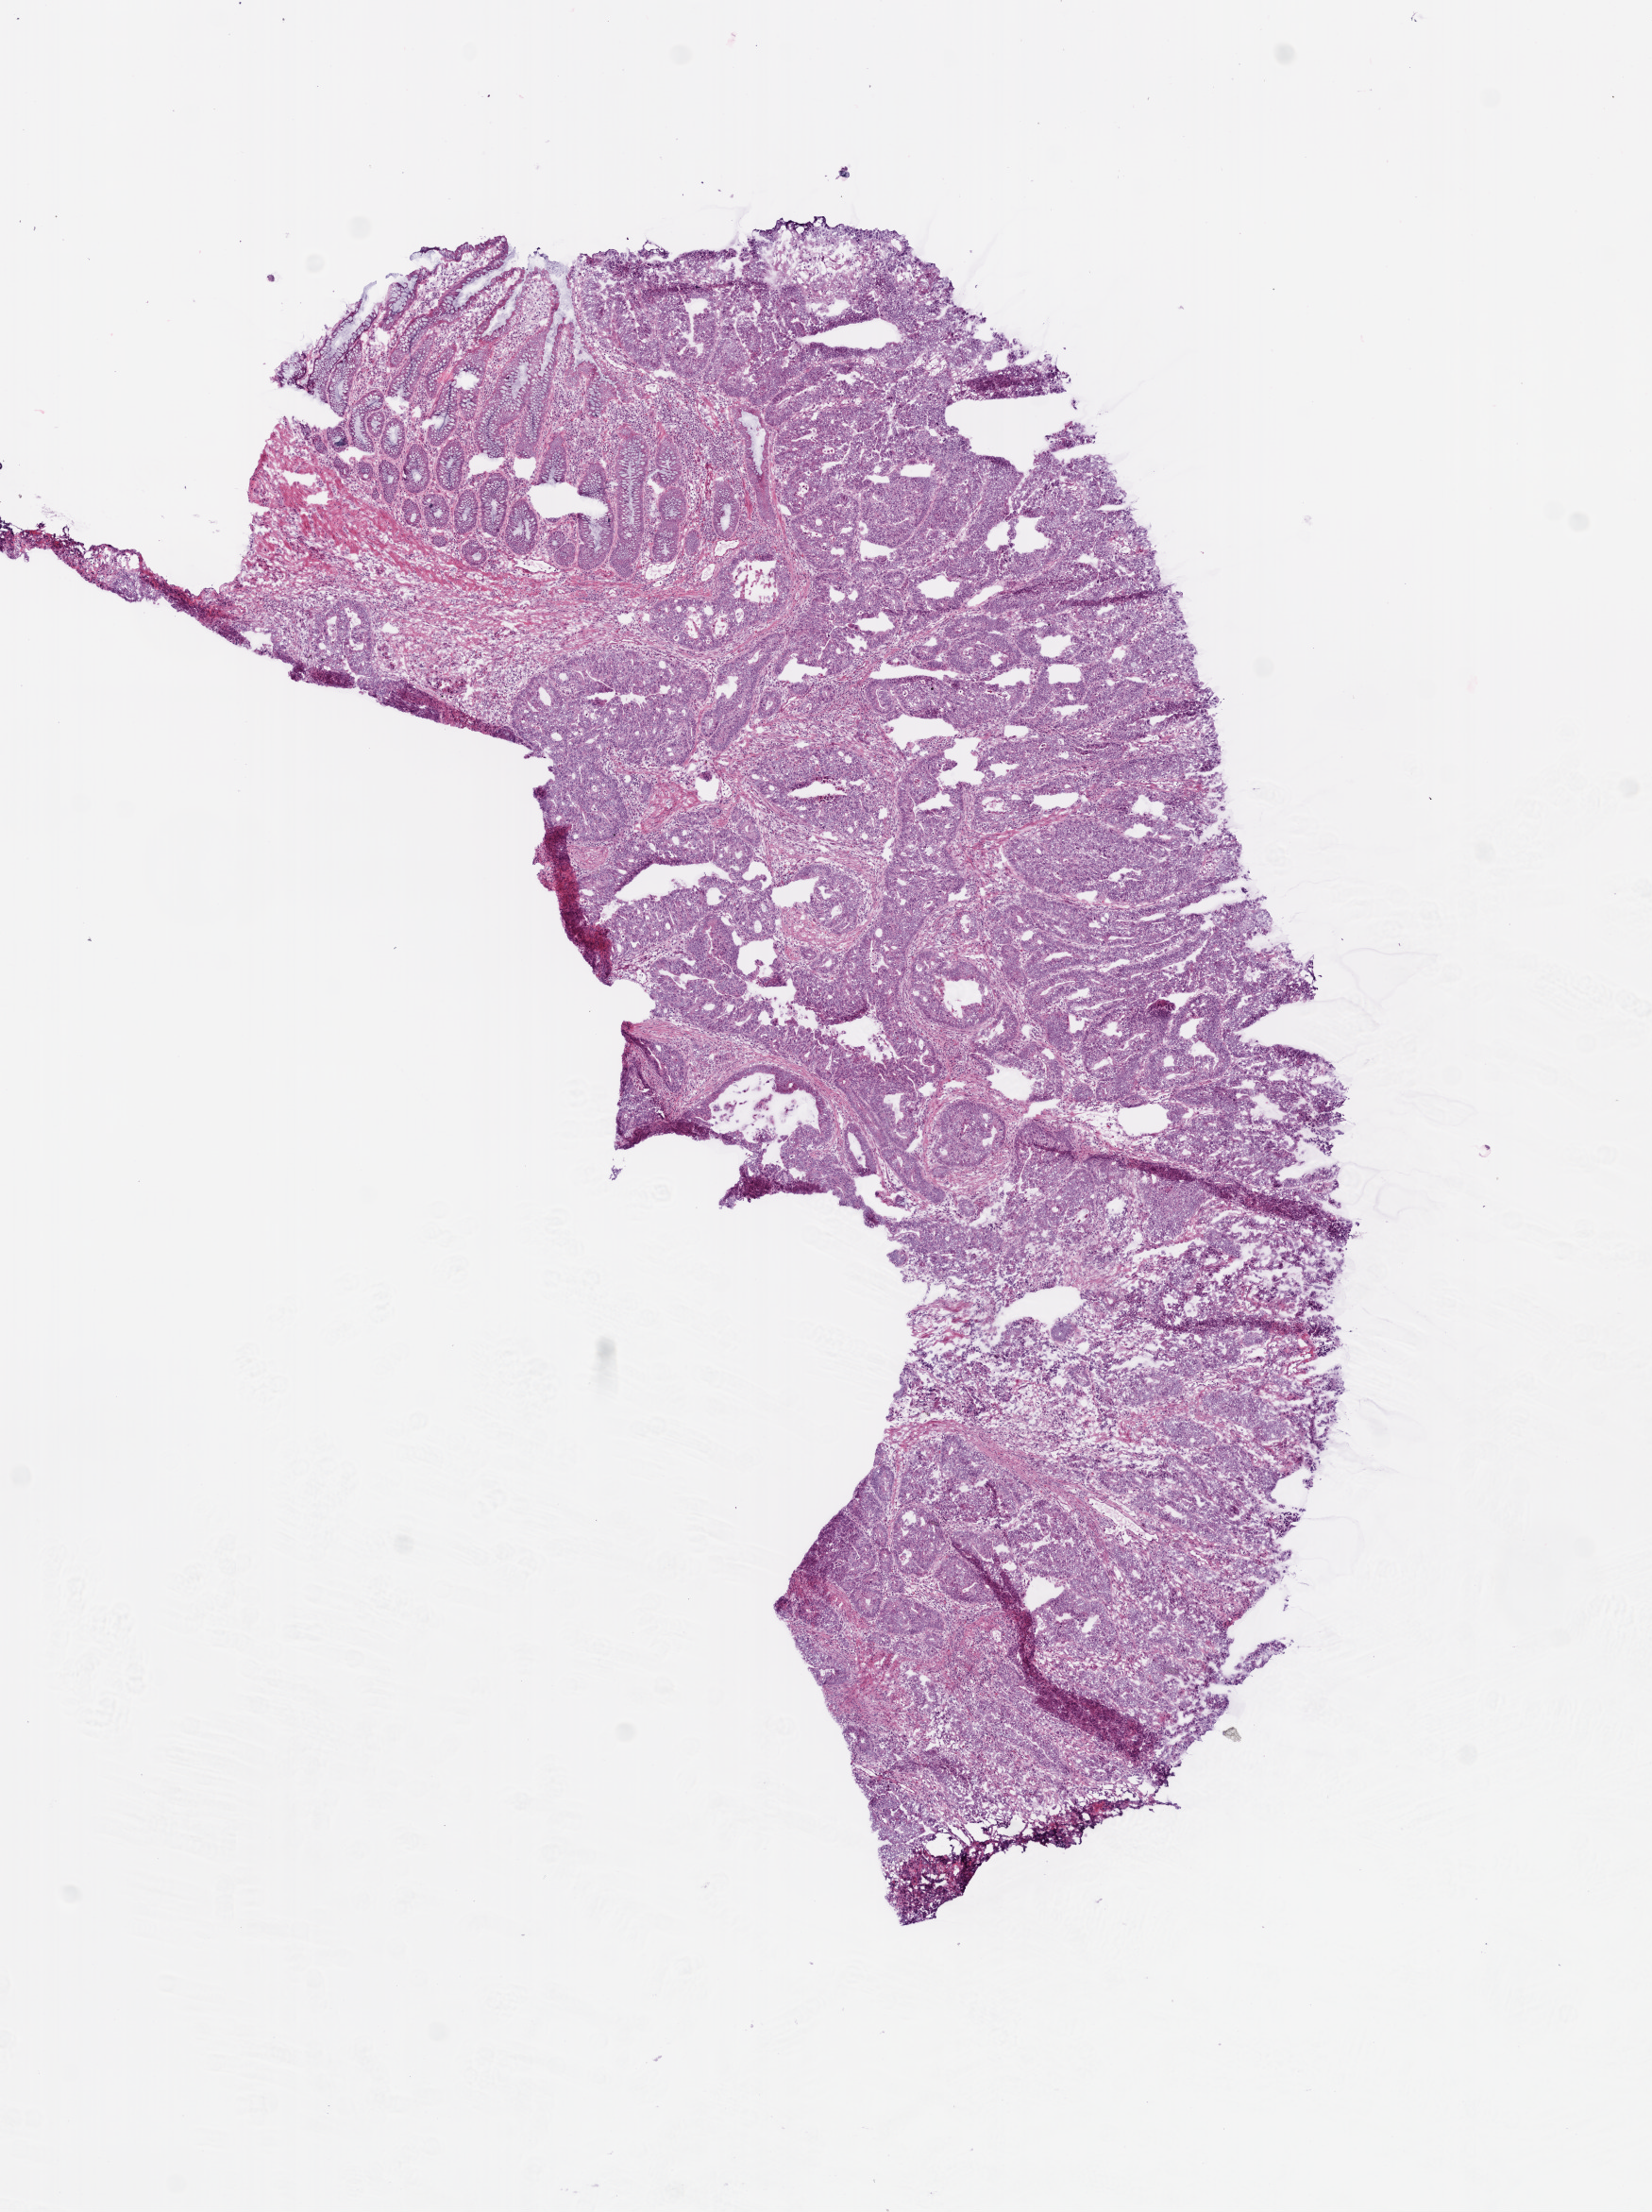
H&E-stained whole-slide image — a low-resolution overview of the entire scanned area, about 7.0 x 9.4 mm, frozen section from the bottom of the tissue portion, colon, primary tumour sample. Patient: male, age at initial diagnosis 67 years. Pathologist review of this section (percent, as recorded): tumour cells 74%, tumour nuclei 85%, normal cells 8%, stromal cells 10%, necrosis 8%.
AJCC pathologic stage: I. TNM: T2 N0 M0. Lymph nodes positive (case pathology): 0 of 12 examined. Diagnosis: Adenocarcinoma, NOS.